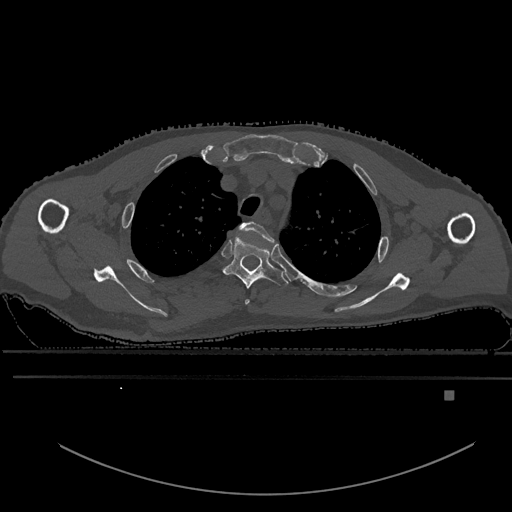
CT including the spine, one axial slice. Slice 459 of 969 in the series (ordered by position). Bone window (W 1800 / L 400 HU). 0.5 mm slice thickness. 512 × 512 image matrix, field of view 456 × 456 mm. Patient: male, 82 years. Case-level facts recorded for this patient, not image findings: primary cancer: prostate; vertebrae with lytic lesions (as recorded): T11, T9, T8, T2.
Annotated regions visible in this slice (semi-automatic segmentation, software-assisted and operator-edited):
- T2 vertebra: bounding box (x1, y1, x2, y2) in pixels: (239, 221, 276, 305)
- T3 vertebra: (223, 237, 289, 289)